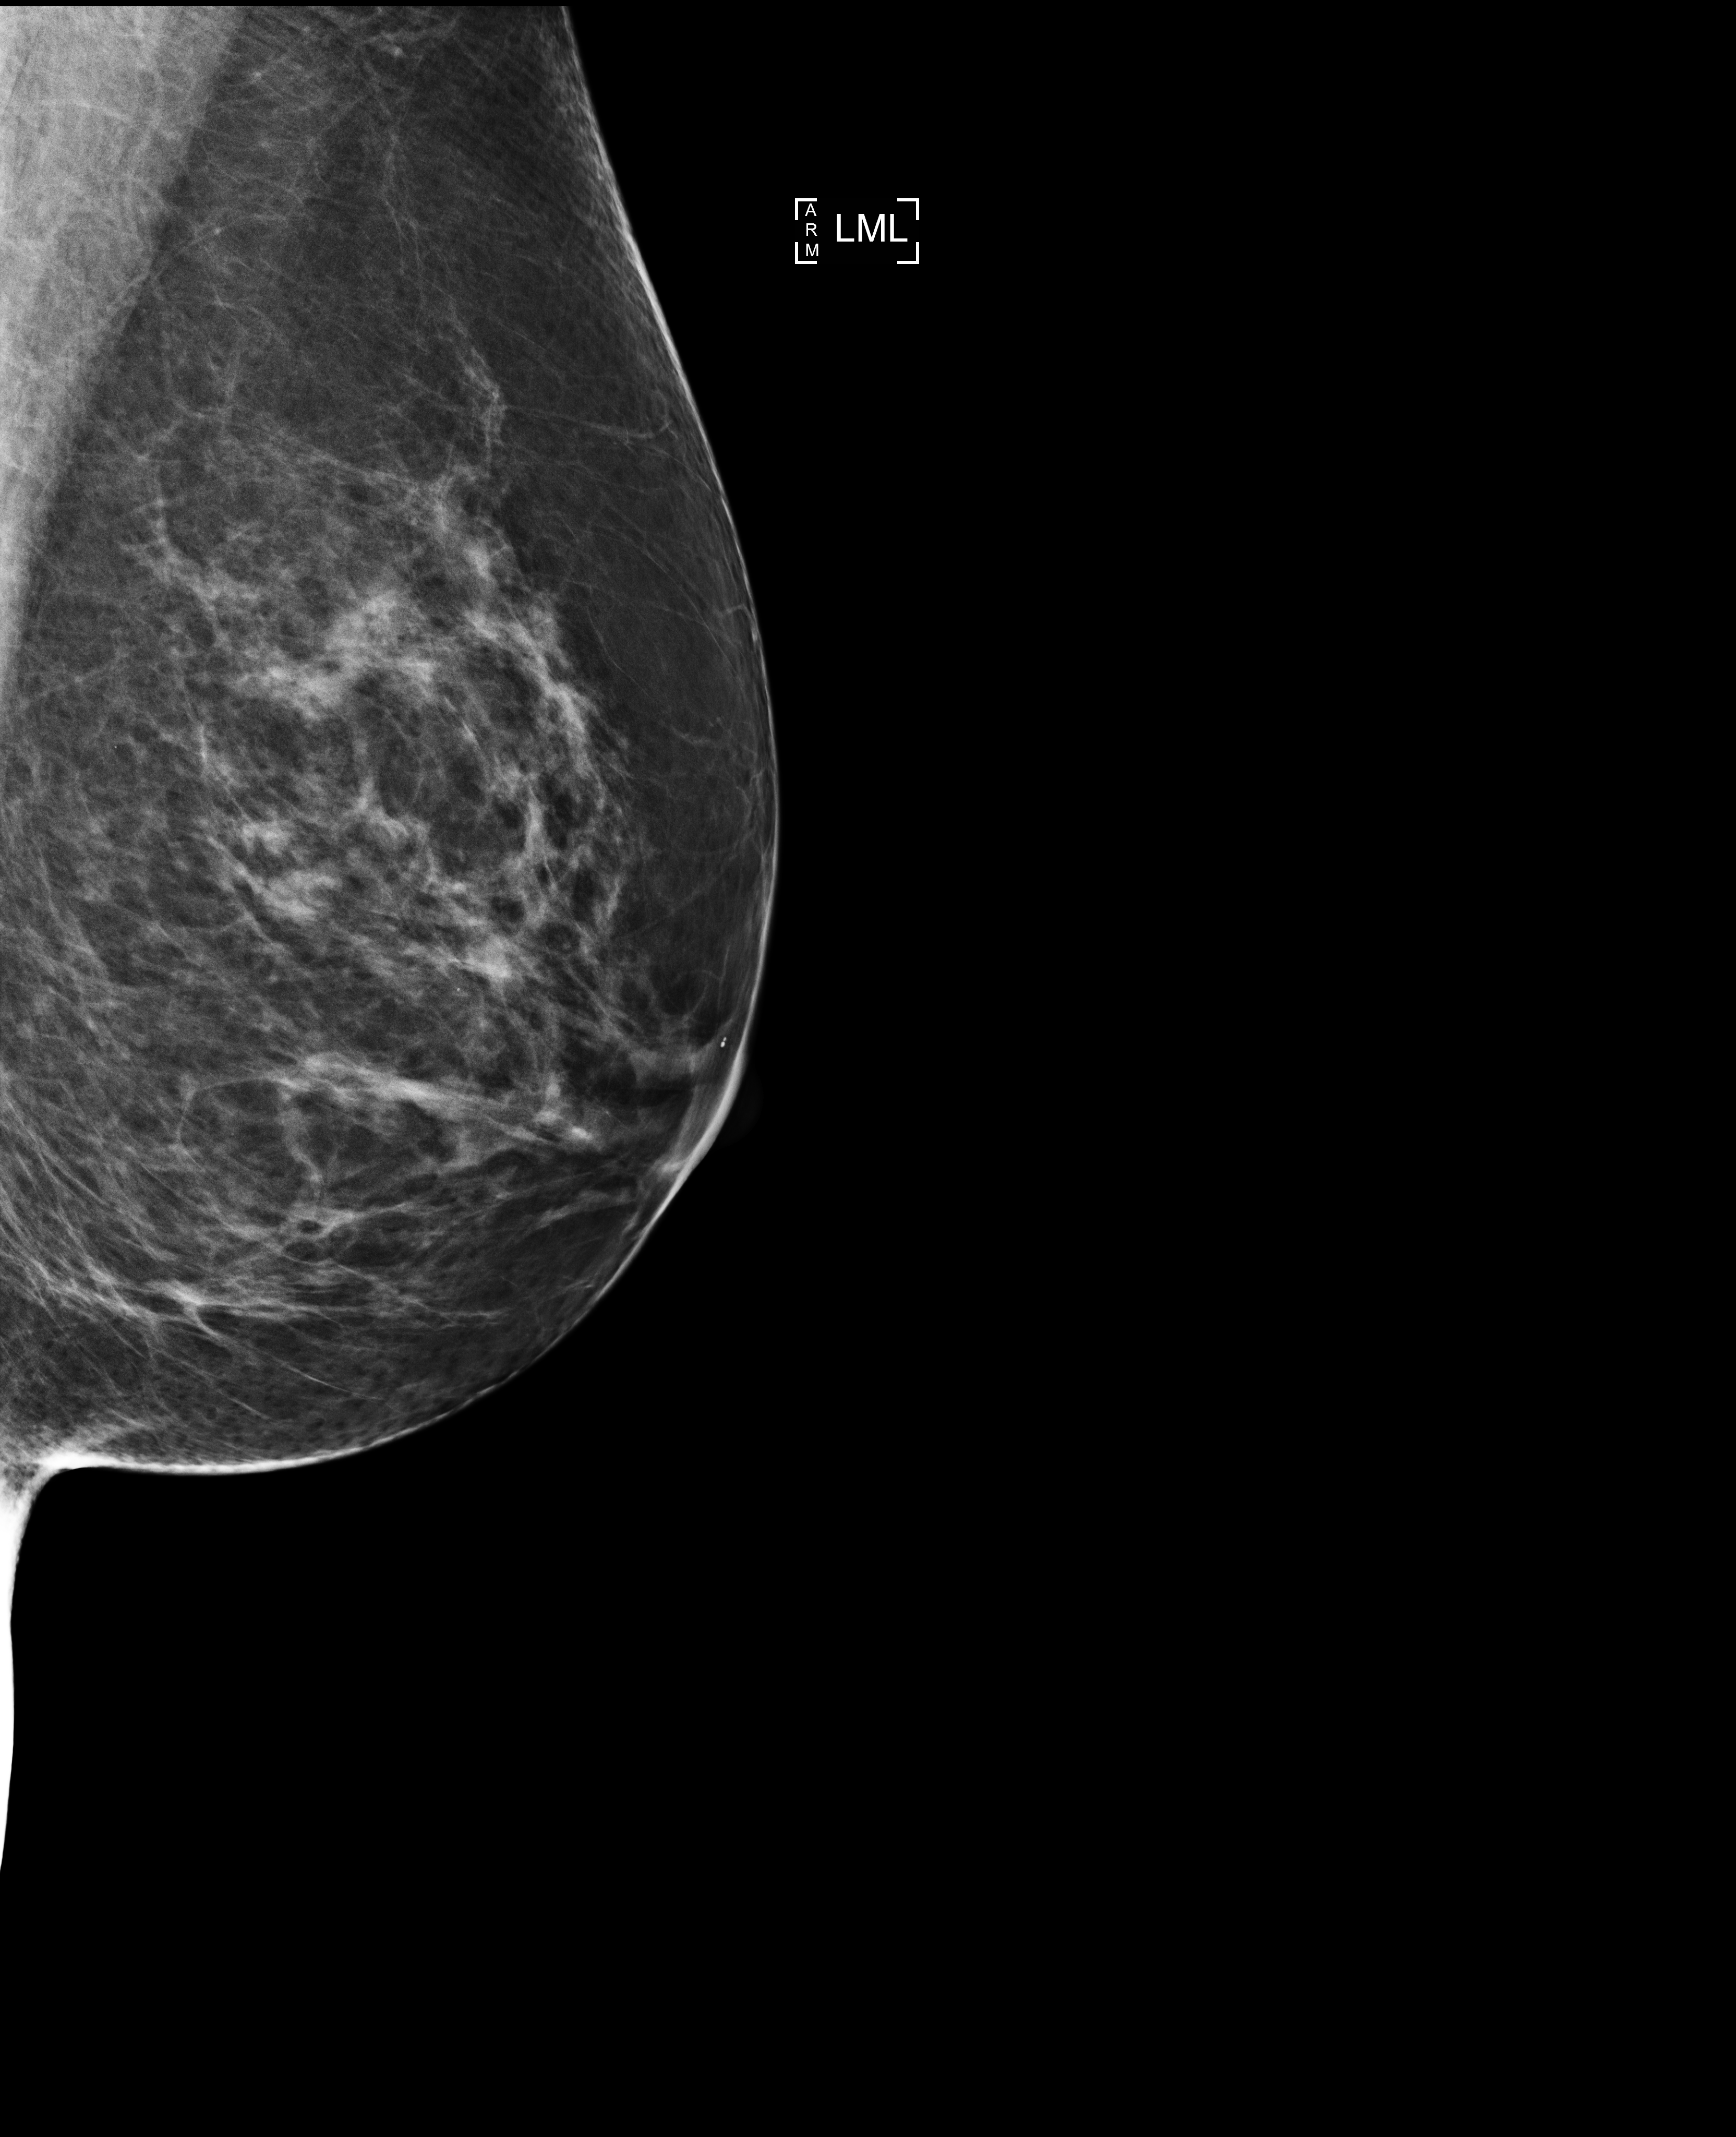
Diagnostic work-up study.
Image type: full-field digital mammogram. Breast: left. Projection: ML view.